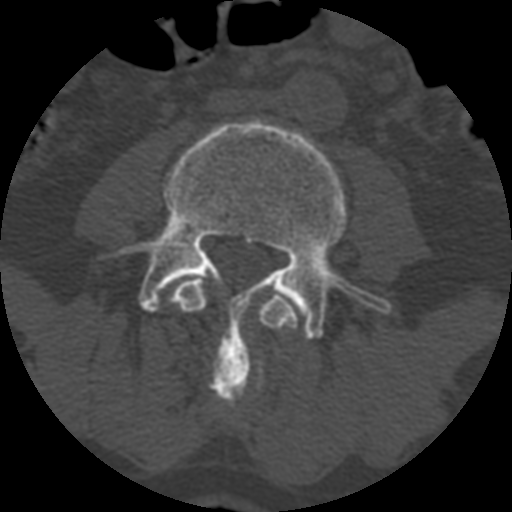
CT including the spine, one axial slice. Position 288 of 399 along the scan axis. 120 kVp. Bone window (W 1800 / L 400 HU). 1.25 mm slice thickness. 512 × 512 image matrix, field of view 160 × 160 mm. Patient age 71 years. From the clinical record (not read from this slice): primary cancer: prostate.
Structures marked on this image (semi-automatically segmented with operator editing):
- L3 vertebra: bounding box <168,277,299,407> (left, top, right, bottom; pixels)
- L4 vertebra: <108,120,391,398>